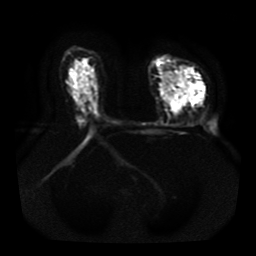
Breast MRI, one axial slice; position 26 of 41 along the scan axis; diffusion-weighted series; image 2 of 4 stored at this slice position (different b-values; order by instance number); 1.5 T; 5 mm slice thickness; 256 × 256 image matrix, field of view 330 × 330 mm. Female patient.
Structures marked on this image (outlined manually by an expert reader):
- tumour on diffusion-weighted imaging: bounding box [x1, y1, x2, y2] px = [159, 69, 204, 113]